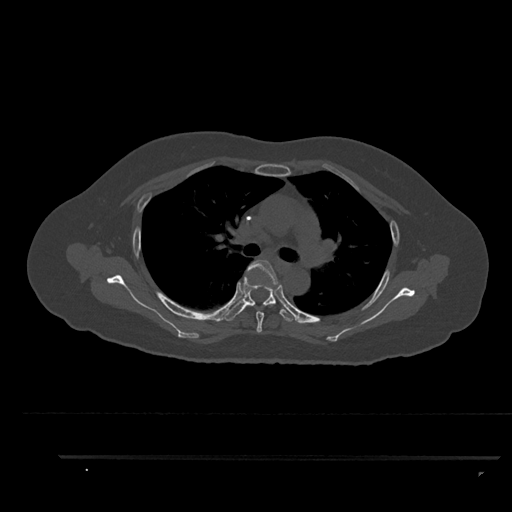
CT including the spine, one axial slice. Position 620 of 797 along the scan axis. Reconstruction kernel Br40s/3. 120 kVp. Bone window (W 1800 / L 400 HU). 512 × 512 image matrix, field of view 408 × 408 mm. Female patient, age 44 years. From the clinical record (not read from this slice): primary cancer: renal.
Structures marked on this image (semi-automatic segmentation, software-assisted and operator-edited):
- T4 vertebra: bounding box <247,260,281,333> (left, top, right, bottom; pixels)
- T5 vertebra: <225,277,297,322>